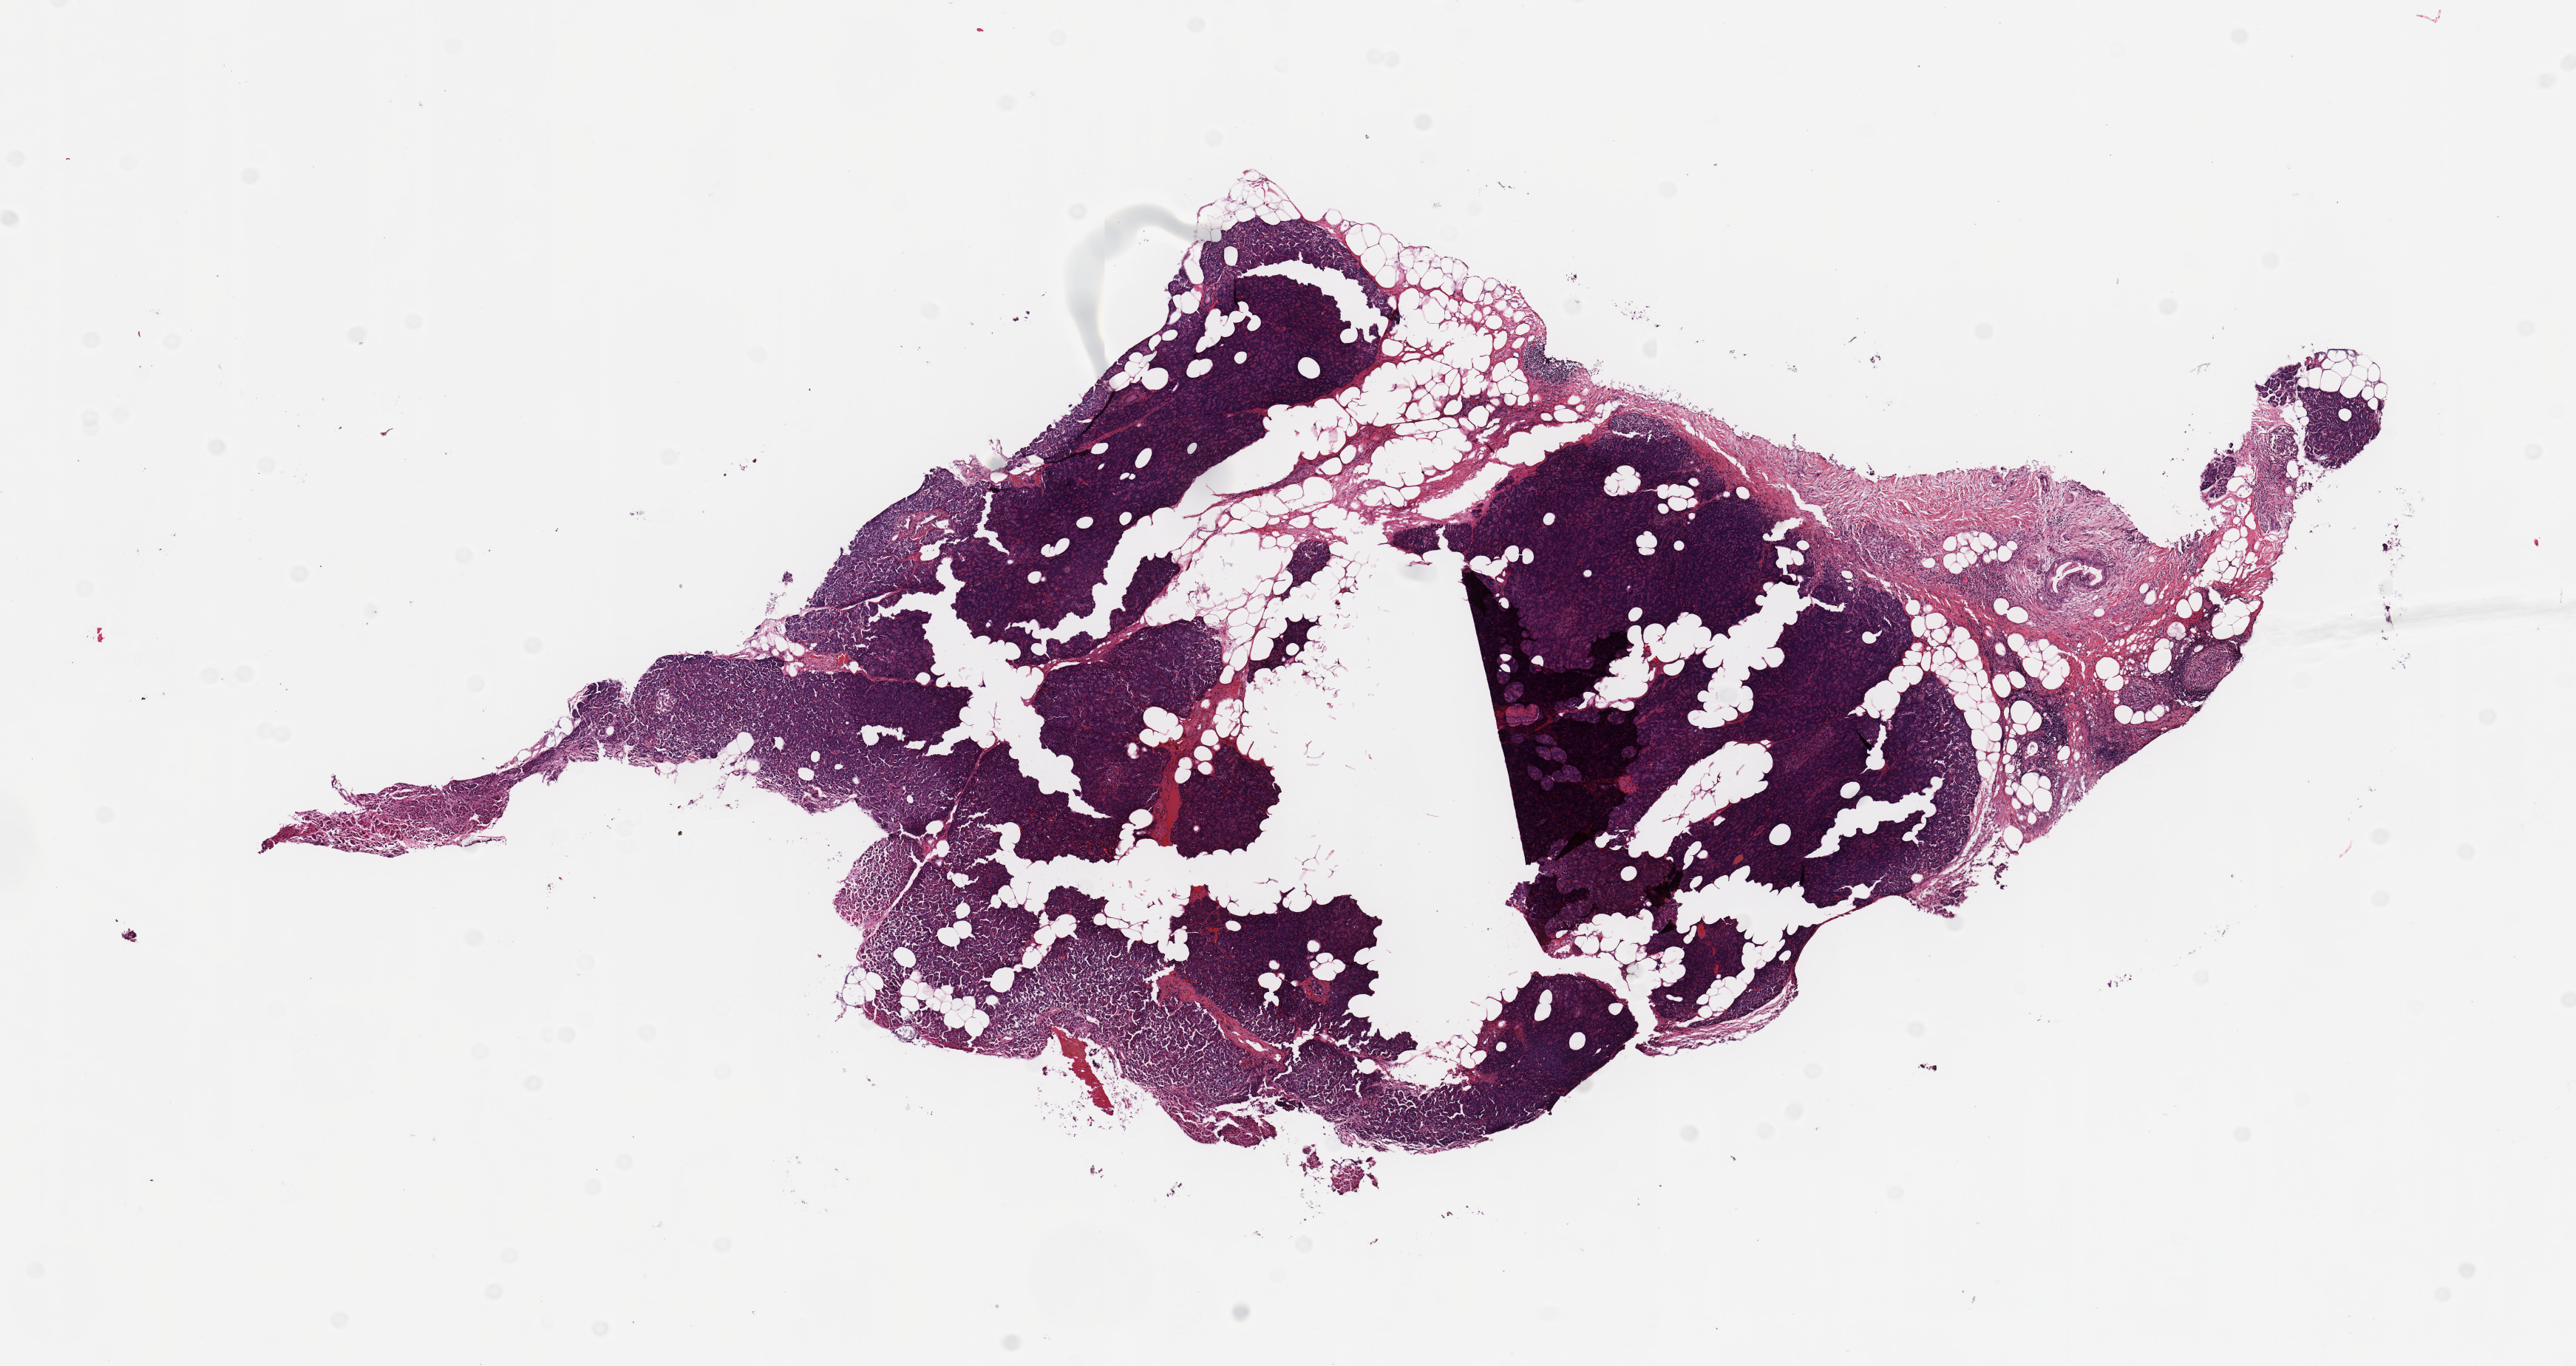
Whole-slide histology image, H&E-stained, low-resolution overview of the scanned area, about 13.8 x 7.3 mm; normal (non-tumour) tissue sample, sampled site: pancreas. Patient: female, age 65 years.
This section: normal (non-tumour) tissue from the same patient. Patient diagnosis: Infiltrating duct carcinoma, NOS.